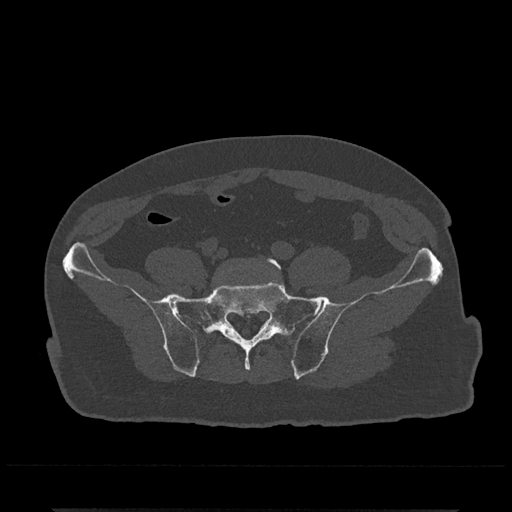
CT including the spine, one axial slice. Position 33 of 797 along the scan axis. Reconstruction kernel Br40s/3. 120 kVp. Bone window (W 1800 / L 400 HU). 512 × 512 image matrix, field of view 393 × 393 mm. Patient: male, 67 years. From the clinical record (not read from this slice): primary cancer: prostate.
Structures marked on this image (semi-automatically segmented with operator editing):
- L5 vertebra: box from (x=267, y=257) to (x=281, y=269) px